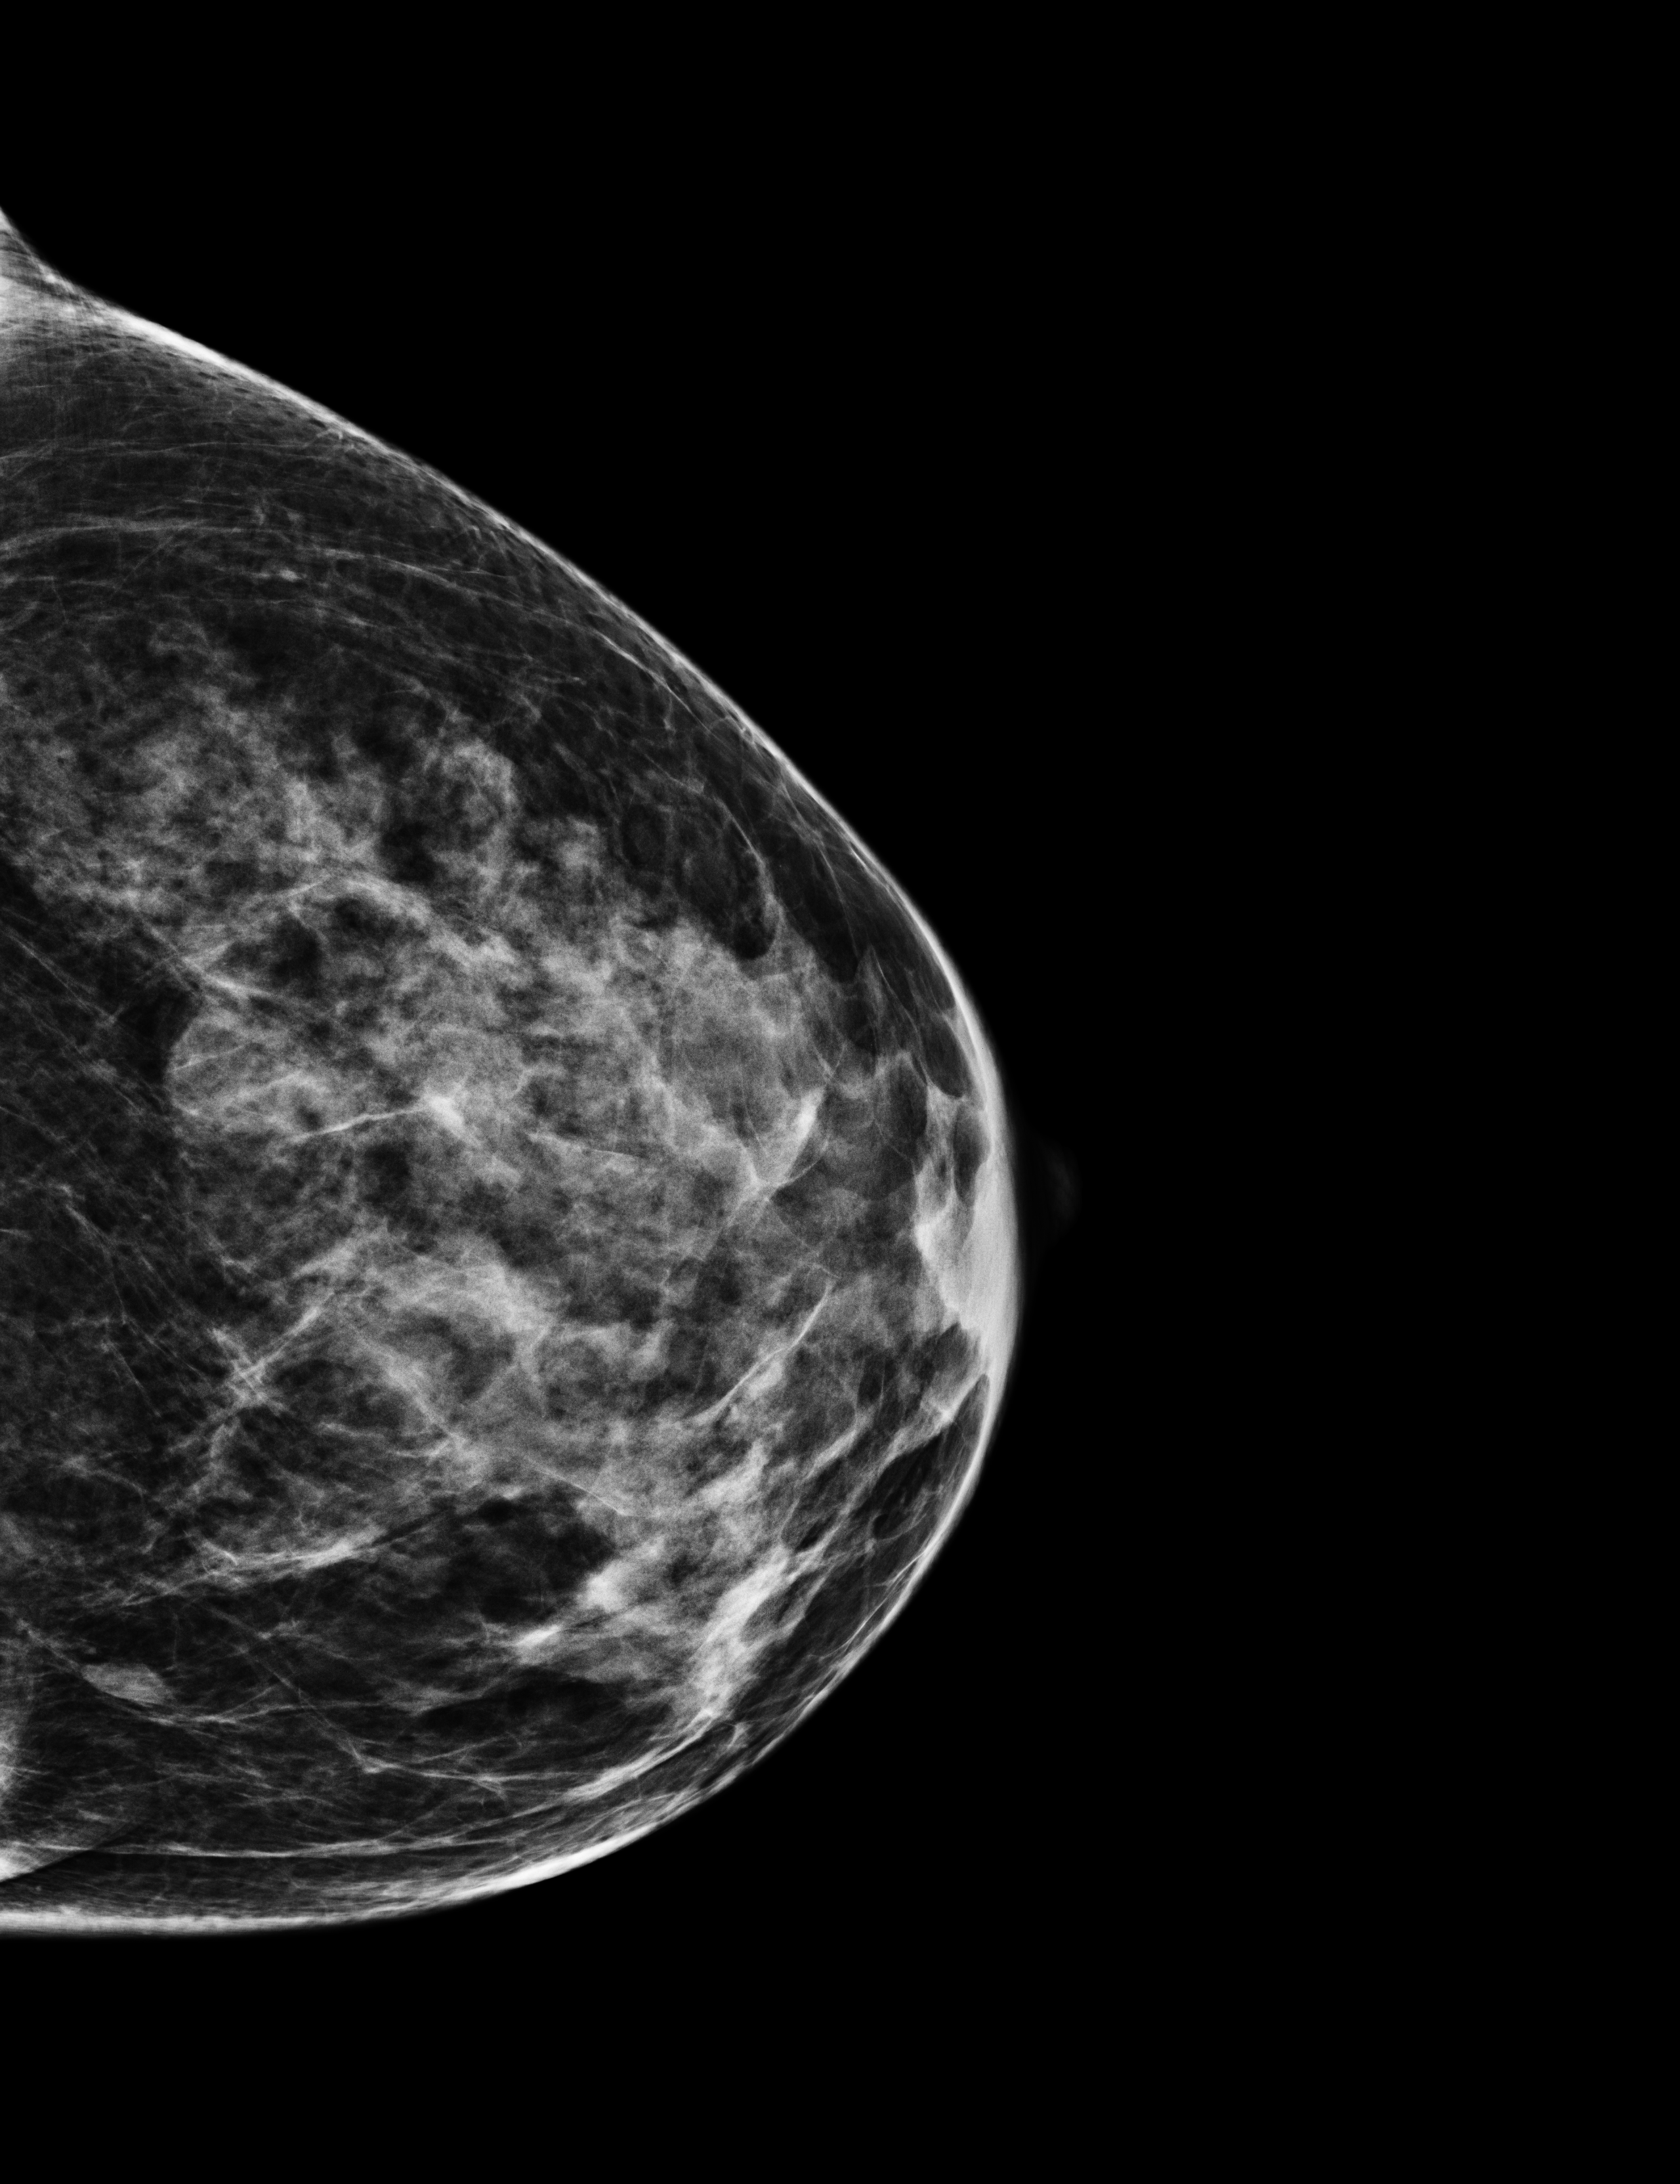
Full-field digital mammogram (FFDM), left breast, CC view, screening examination, compressed breast thickness 51 mm. Patient: female, 62 years.
Breast density at the screening exam (both breasts): heterogeneously dense (BI-RADS density category c). Final BI-RADS assessment for this screening round (tomosynthesis exam, both breasts): category 2. Recall: no recall after this screen.